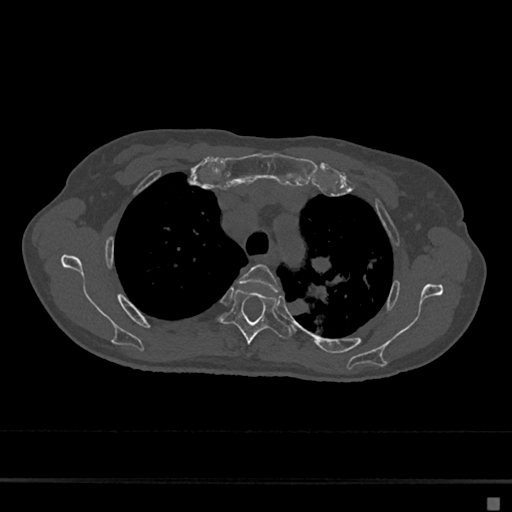
CT including the spine, one axial slice. Slice 510 of 797 in the series (ordered by position). 120 kVp. Bone window (W 1800 / L 400 HU). 0.5 mm slice thickness. 512 × 512 image matrix, field of view 360 × 360 mm. Female patient, age 68 years. From the clinical record (not read from this slice): primary cancer: renal.
Annotated regions visible in this slice (semi-automatically segmented with operator editing):
- T3 vertebra: box from (x=238, y=264) to (x=279, y=293) px
- T4 vertebra: (x=220, y=288)–(x=292, y=344)